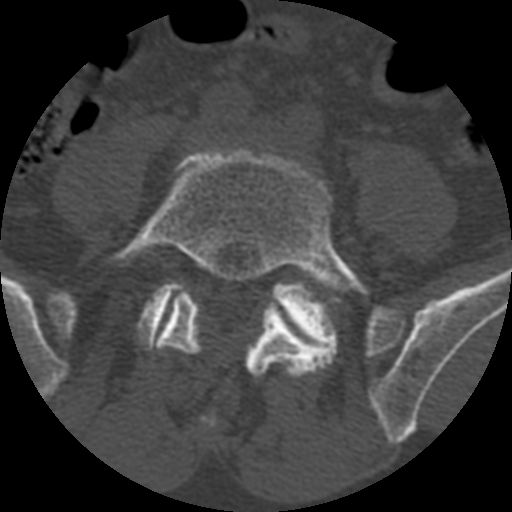
CT including the spine, one axial slice; slice 254 of 399 in the series (ordered by position); bone window (W 1800 / L 400 HU); 1.25 mm slice thickness; 512 × 512 image matrix, field of view 160 × 160 mm. Patient age 71 years. From the clinical record (not read from this slice): primary cancer: prostate.
Structures marked on this image (semi-automatic segmentation, software-assisted and operator-edited):
- L5 vertebra: bounding box [x1, y1, x2, y2] px = [107, 147, 373, 379]